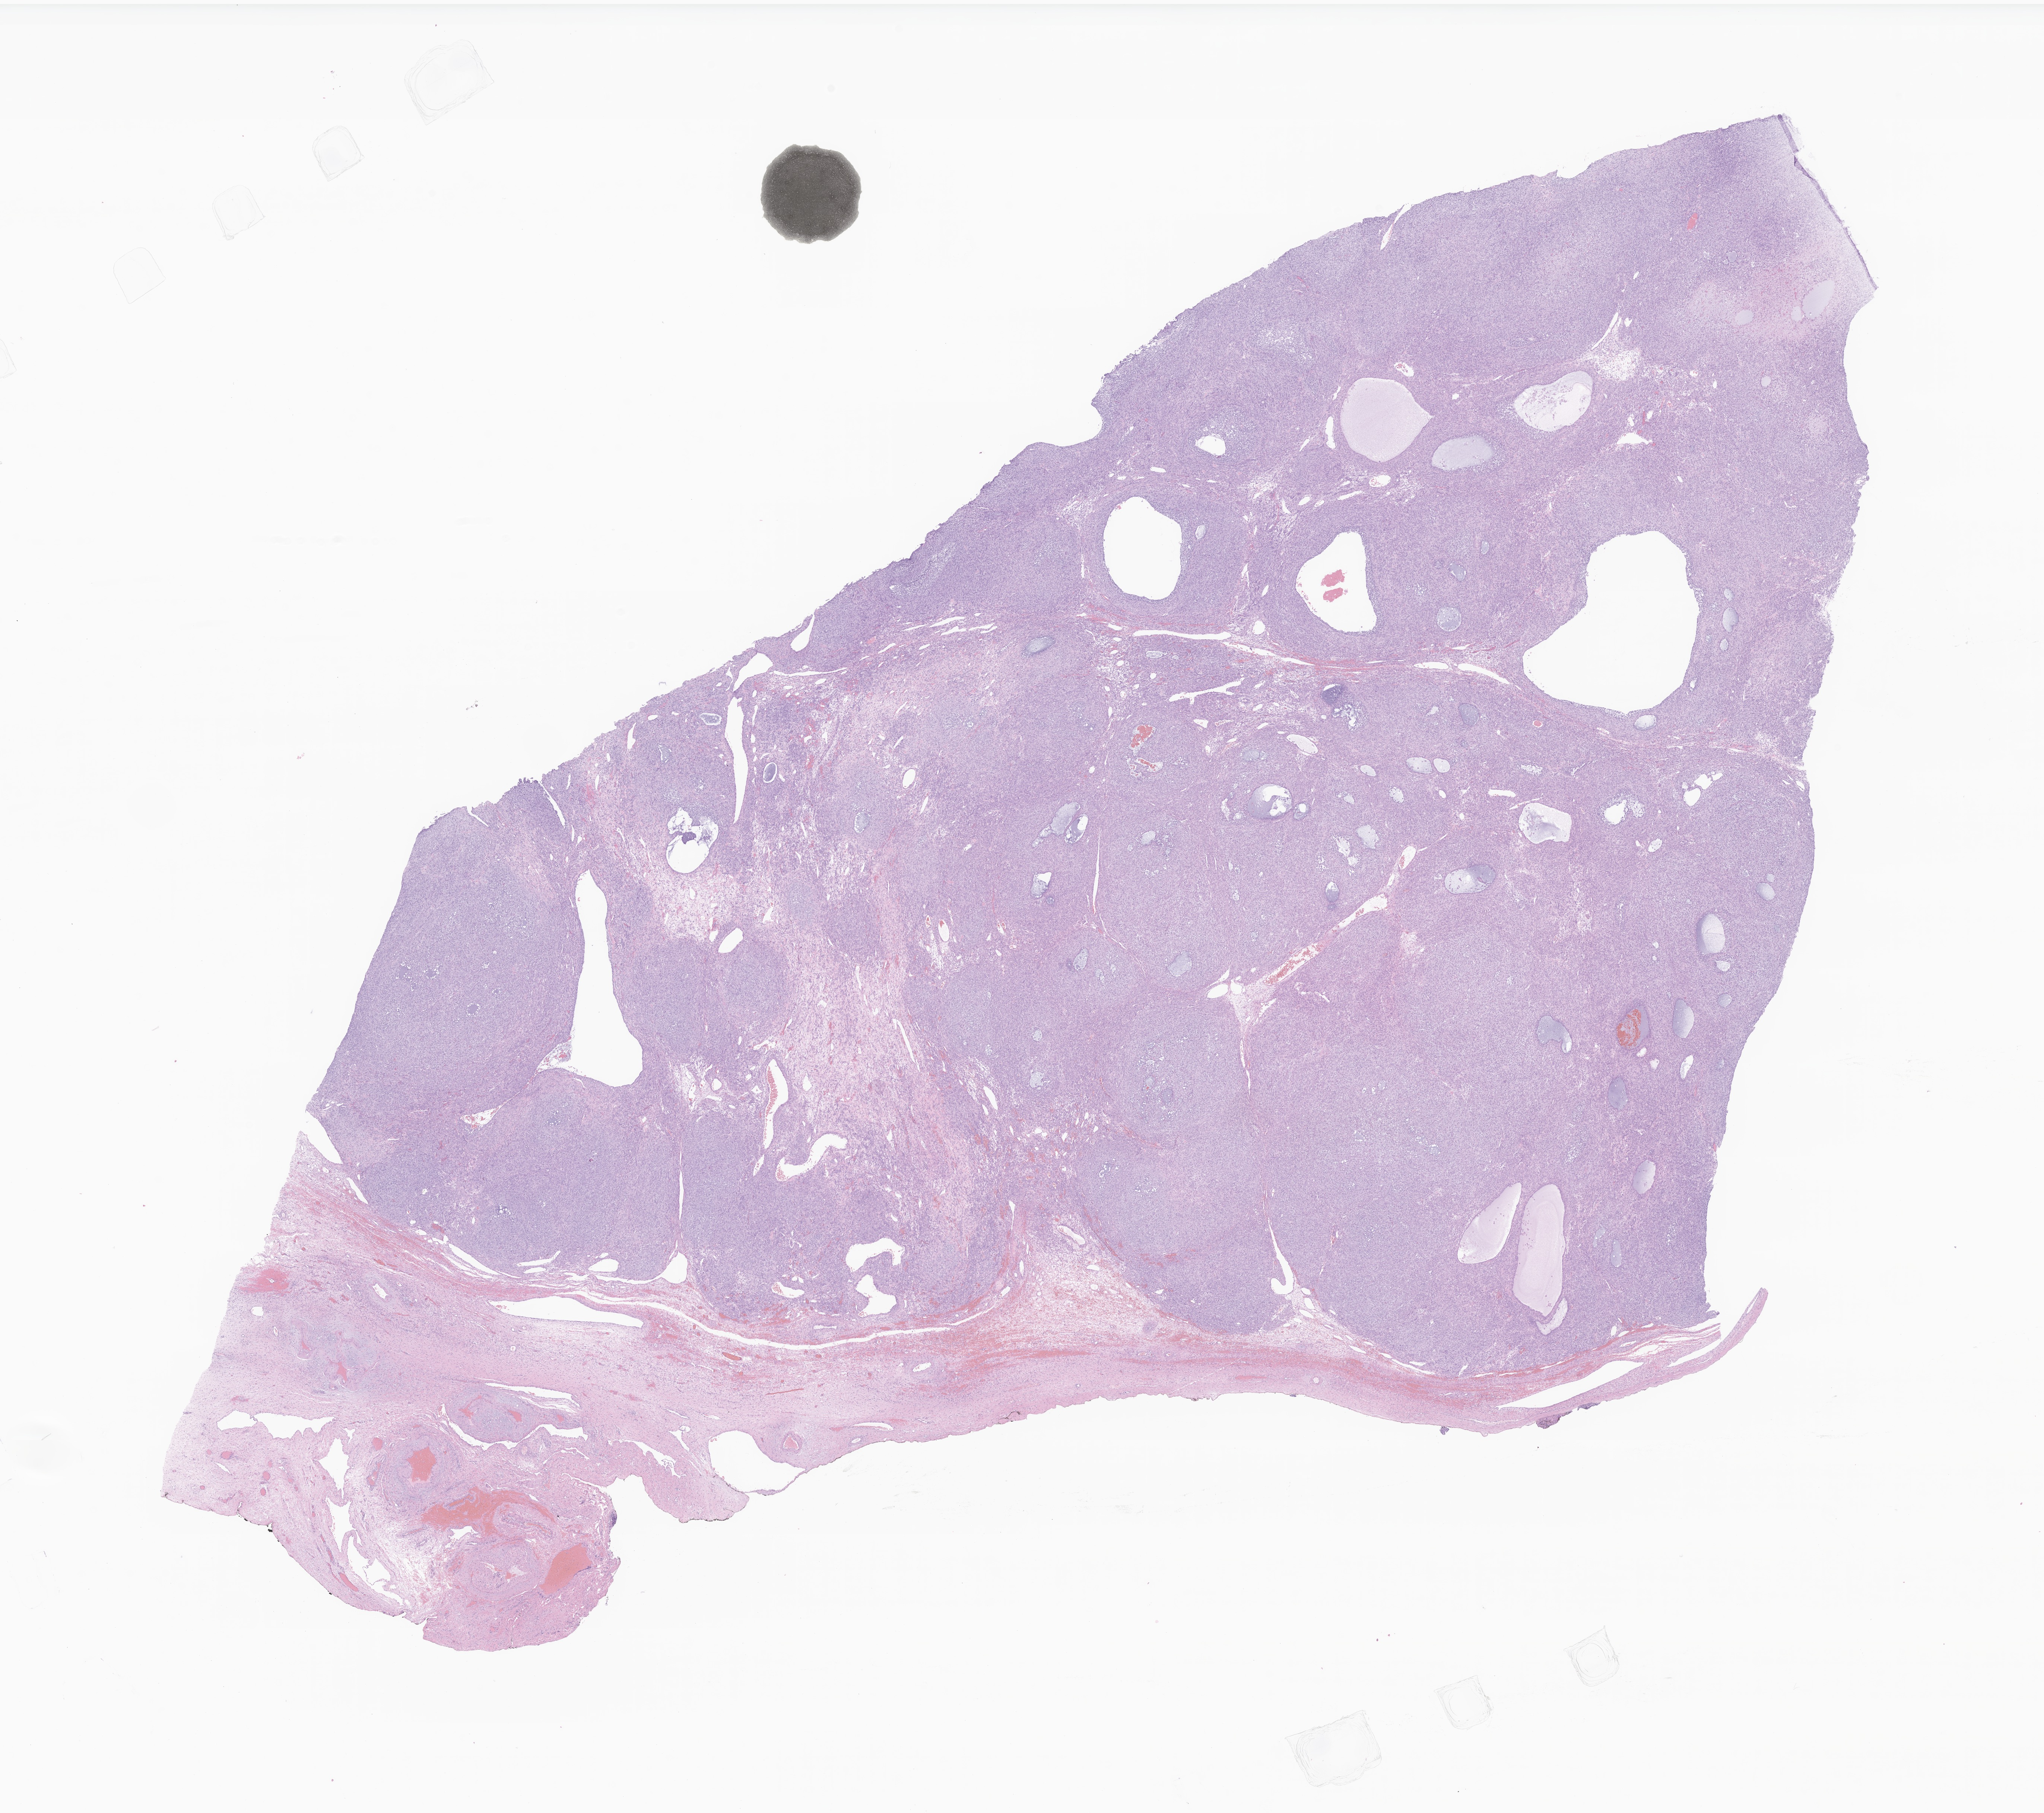
Hematoxylin and eosin (H&E) whole-slide image of tumor tissue from the ovary — whole scanned area (about 23.1 x 20.5 mm) shown as a low-resolution overview. Formalin-fixed paraffin-embedded section. Female patient, age 815 days (about 2.2 years).
Diagnosis: Granulosa cell tumor, juvenile.